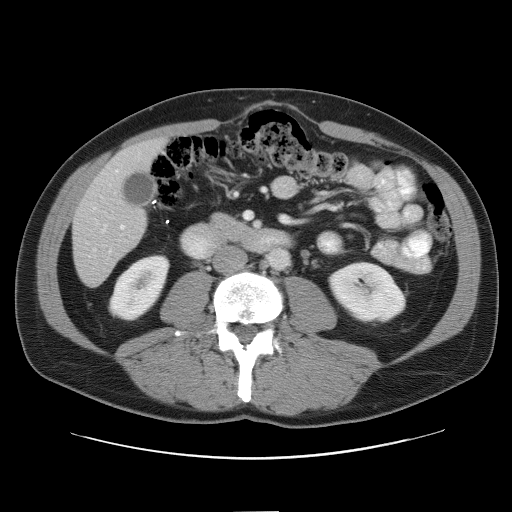
Contrast-enhanced abdominal CT, one axial slice. Position 19 of 52 along the scan axis. Intravenous contrast given. Soft-tissue window (W 400 / L 40 HU). 512 × 512 image matrix, field of view 393 × 393 mm. Male patient, age 70 years. Case-level facts recorded for this patient, not image findings: diagnosis: colorectal cancer liver metastases, imaged before liver resection; multiple liver metastases: yes; largest metastasis: 4 cm; disease in both lobes: yes.
Annotated regions visible in this slice (outlined manually by an expert reader):
- hepatic veins: bounding box <103,226,106,232> (left, top, right, bottom; pixels)
- liver: <73,140,163,286>
- planned liver remnant (the part of the liver to remain after resection): <118,140,163,173>
- portal vein (with intrahepatic branches): <120,224,125,230>